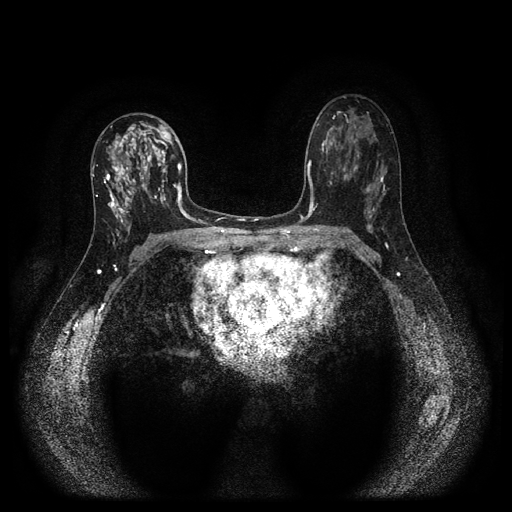
Breast MRI (dynamic contrast-enhanced, multi-phase), one axial slice. Position 58 of 116 along the scan axis. Dynamic contrast-enhanced series, time point 2 of 5 at this slice position (early post-contrast). 1.5 T. TE 2.7 ms, TR 5.4 ms. 512 × 512 image matrix, field of view 330 × 330 mm. Patient: female, 47 years.
Outlined on this slice (semi-automatically segmented with operator editing):
- breast lesion (labelled 'tumour' in the annotation; benign lesions carry a separate 'benign' label): box from (x=96, y=120) to (x=171, y=232) px